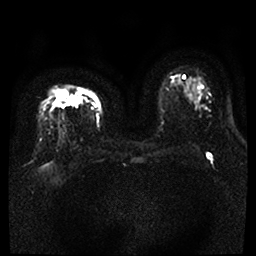
Breast MRI, one axial slice. Position 25 of 46 along the scan axis. Diffusion-weighted series; image 2 of 4 stored at this slice position (different b-values; order by instance number). 1.5 T. 4 mm slice thickness. 256 × 256 image matrix, field of view 360 × 360 mm. Female patient.
Annotated regions visible in this slice (expert manual segmentation):
- tumour on diffusion-weighted imaging: bounding box (x1, y1, x2, y2) in pixels: (55, 91, 82, 107)